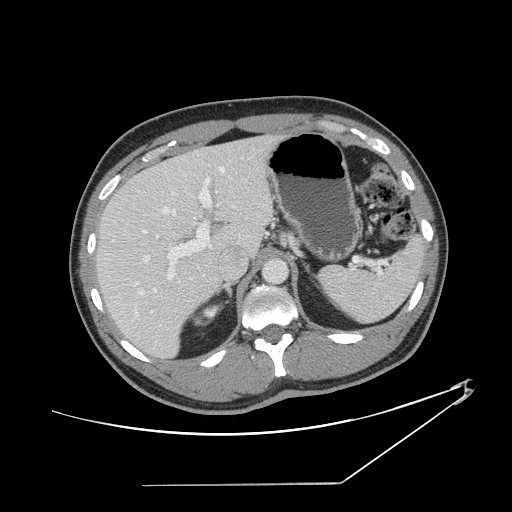
Contrast-enhanced abdominal CT, one axial slice. Slice 94 of 152 in the series (ordered by position). Reconstruction kernel STANDARD. 120 kVp. Soft-tissue window (W 400 / L 40 HU). 2.5 mm slice thickness. 512 × 512 image matrix, field of view 432 × 432 mm. Male patient, age 45 years. Case-level facts recorded for this patient, not image findings: diagnosis: colorectal cancer liver metastases, imaged before liver resection; multiple liver metastases: no; largest metastasis: 1 cm; disease in both lobes: no.
Outlined on this slice (outlined manually by an expert reader):
- hepatic veins: box from (x=111, y=161) to (x=236, y=295) px
- liver: (x=98, y=137)–(x=273, y=357)
- planned liver remnant (the part of the liver to remain after resection): (x=98, y=154)–(x=228, y=357)
- portal vein (with intrahepatic branches): (x=142, y=177)–(x=211, y=326)